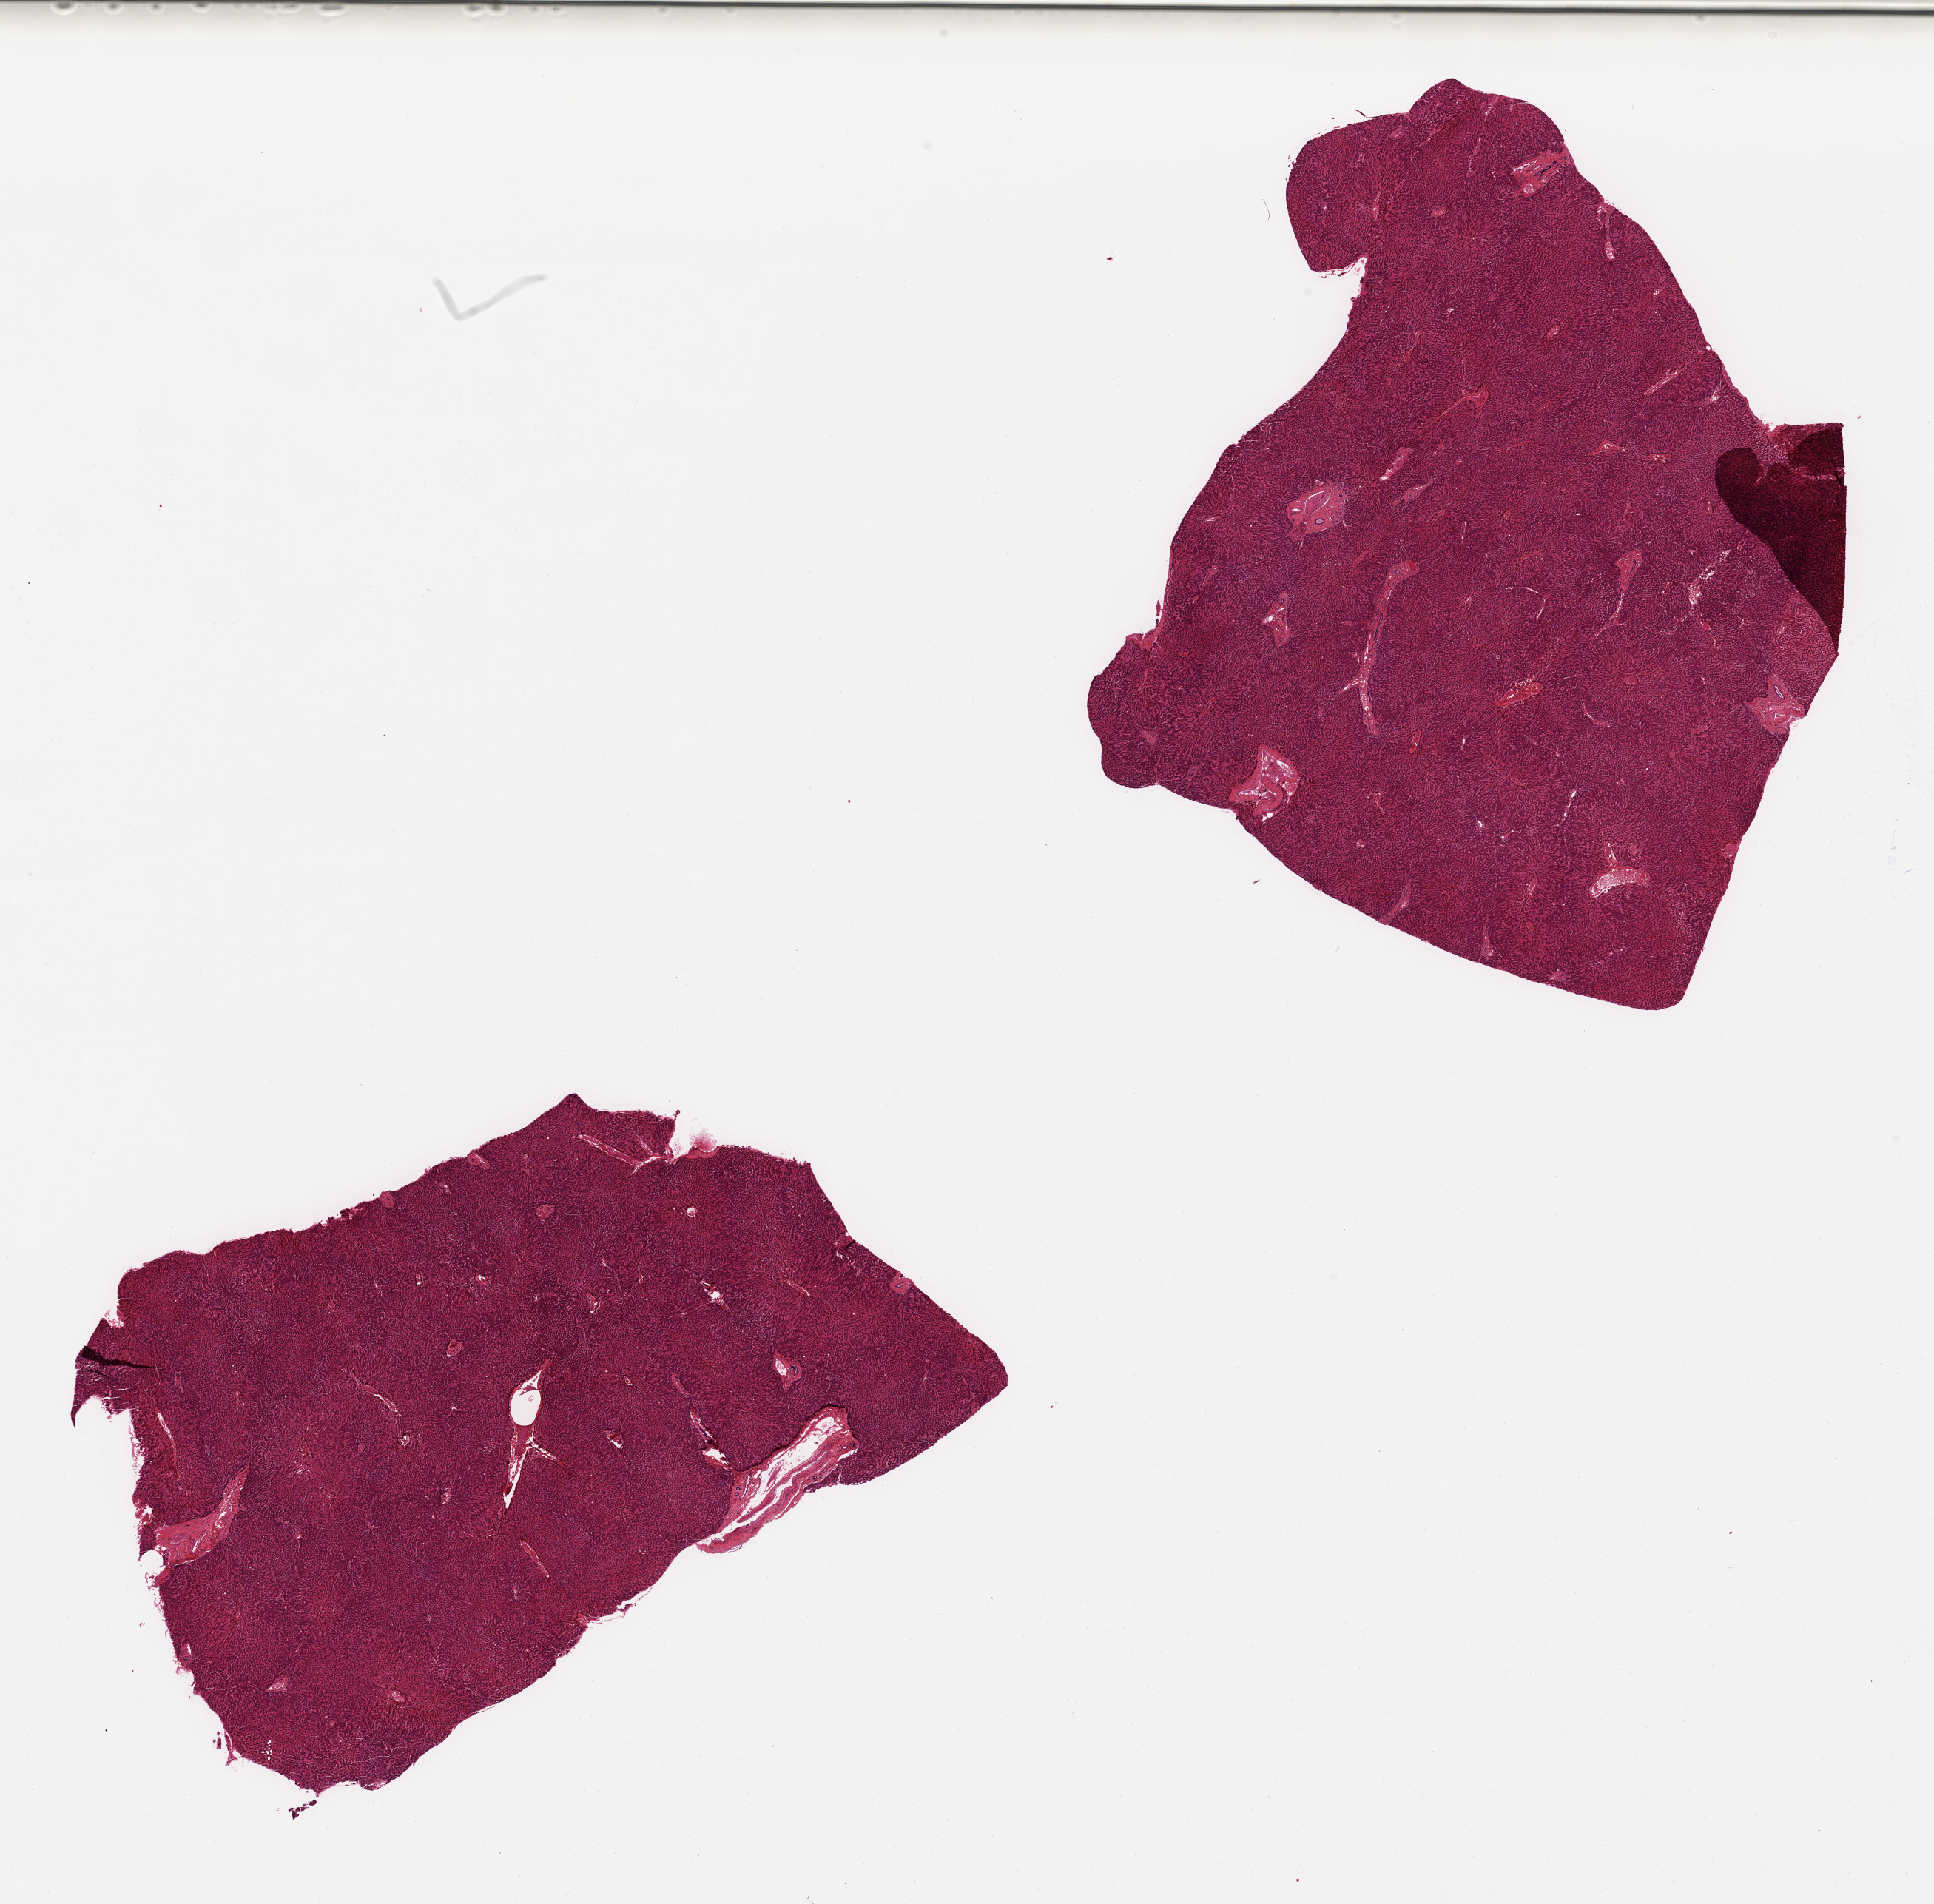
H&E whole-slide image, low-resolution overview of the scanned area, about 20.7 x 20.3 mm (slide scanned at 20x); PAXgene-fixed paraffin-embedded (PFPE) section; section of liver (target tissue); tissue donor sample. Donor sex: female.
Reviewer comment on this tissue sample: 2 pieces ~8x7mm; mild steatosis.